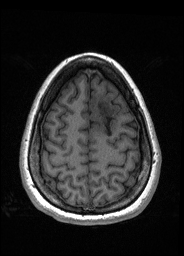
Pre-operative brain MRI before brain-tumour surgery, one axial slice. Position 49 of 176 along the scan axis. T1-weighted post-contrast. 1 mm slice thickness. 184 × 256 image matrix, field of view 180 × 250 mm. From the clinical record (not read from this slice): histopathology: Oligodendroglioma; WHO grade: 2; IDH mutation: yes; tumour location: Left Frontal.
Annotated regions visible in this slice (manually delineated by an expert):
- tumour: bounding box (x1, y1, x2, y2) in pixels: (91, 99, 117, 134)